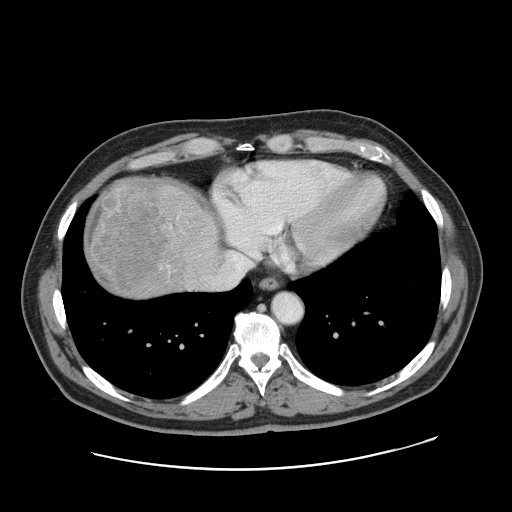
Contrast-enhanced abdominal CT, one axial slice; position 149 of 178 along the scan axis; intravenous contrast given; soft-tissue window (W 400 / L 40 HU); 2.5 mm slice thickness; 512 × 512 image matrix, field of view 403 × 403 mm. Male patient, age 63 years. From the clinical record (not read from this slice): diagnosis: colorectal cancer liver metastases, imaged before liver resection; multiple liver metastases: yes; largest metastasis: 8 cm; disease in both lobes: yes.
Annotated regions visible in this slice (manually delineated by an expert):
- liver: box from (x=83, y=178) to (x=222, y=299) px
- planned liver remnant (the part of the liver to remain after resection): (x=186, y=193)–(x=221, y=253)
- liver metastasis: (x=87, y=183)–(x=165, y=292)